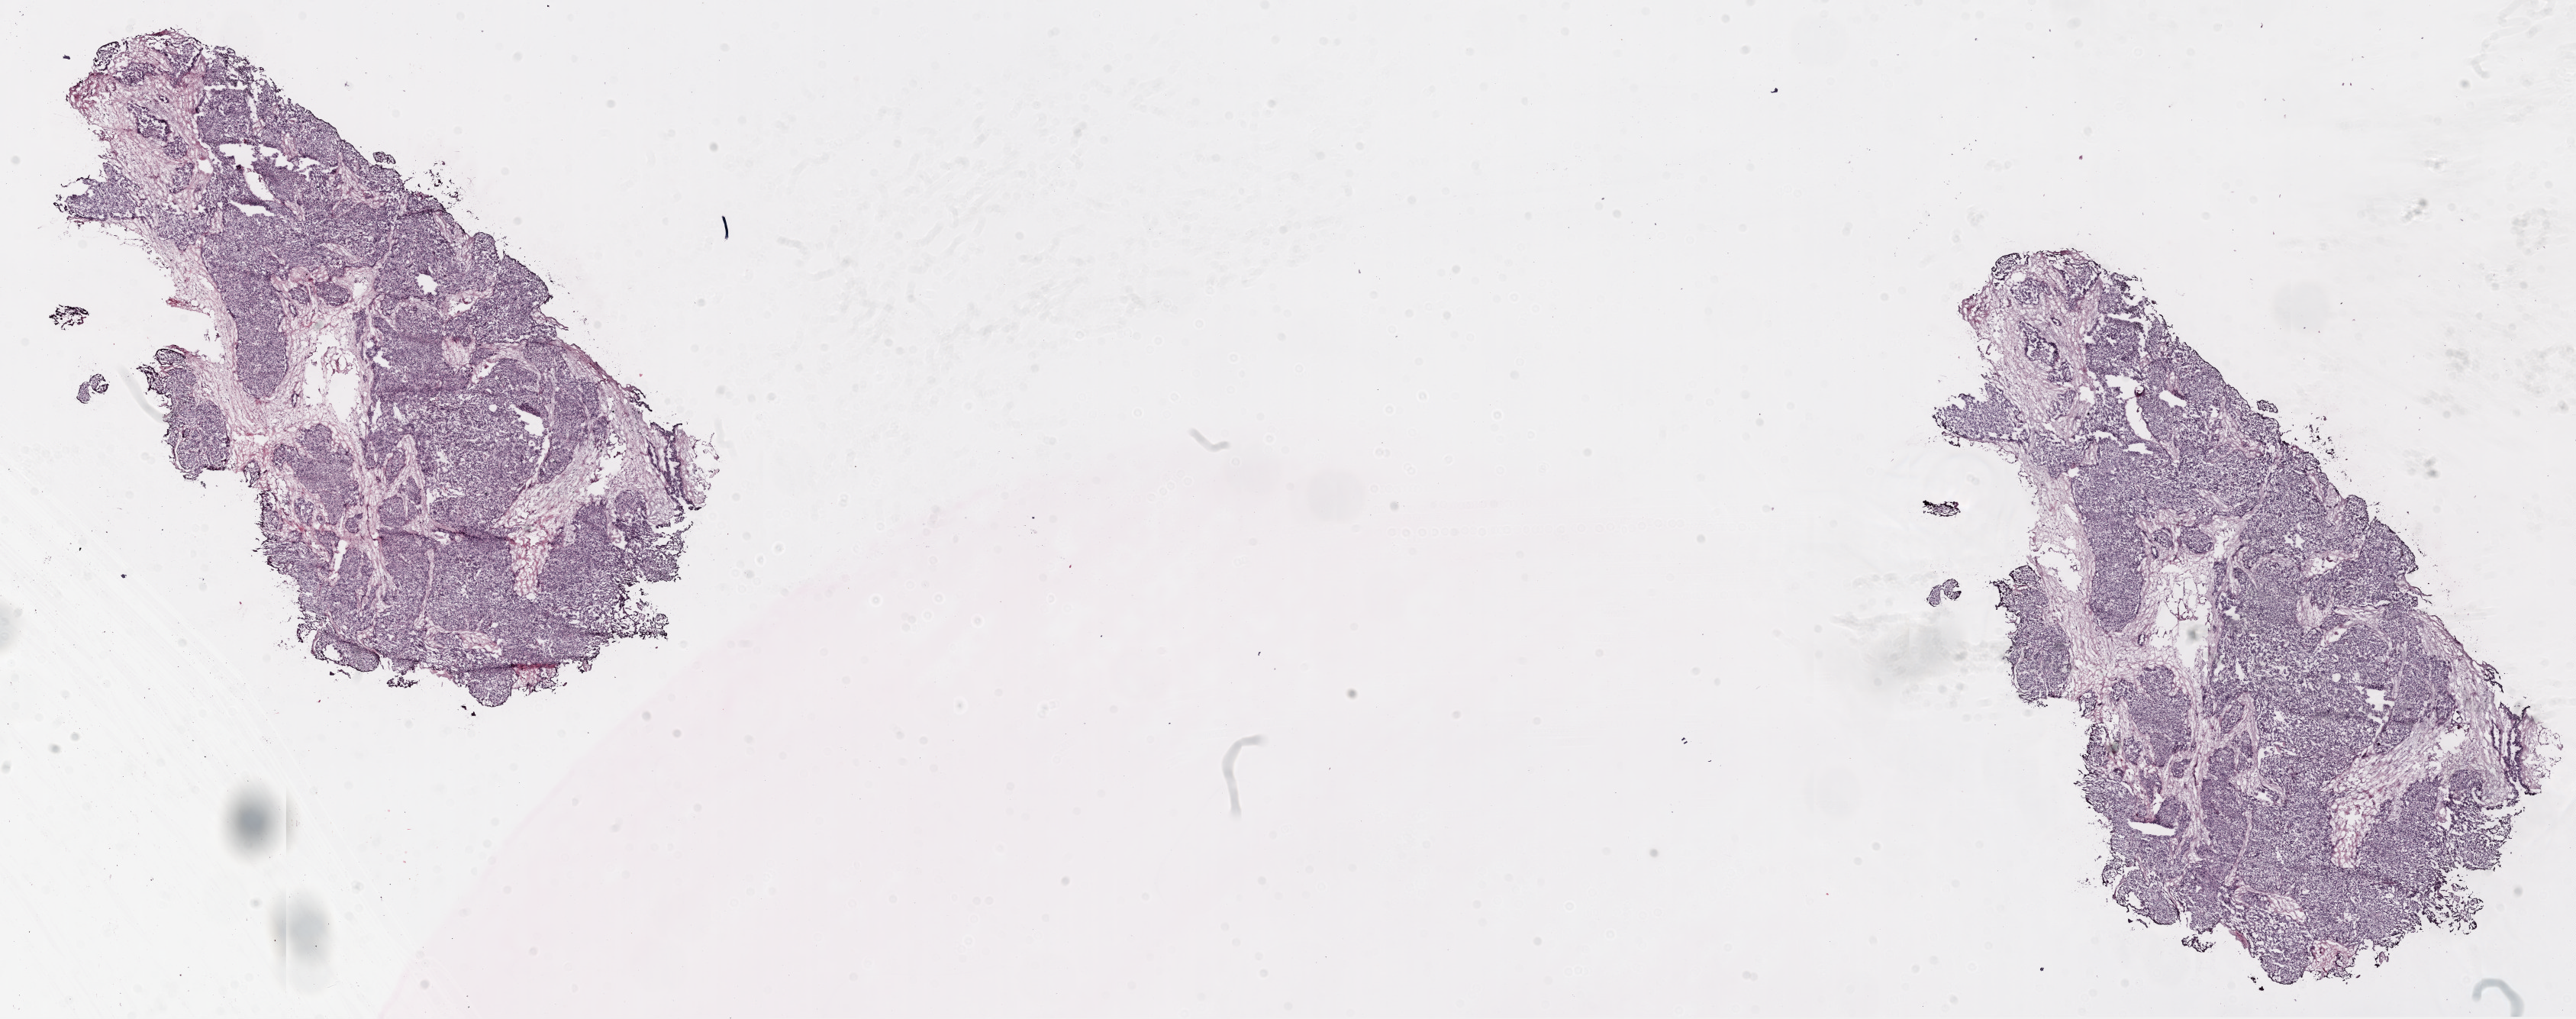
H&E whole-slide image — a low-resolution overview of the entire scanned area, about 27.1 x 10.7 mm (acquisition: 20x scan), frozen section from the top of the tissue portion, ovary, primary tumour sample. Female patient; age at initial diagnosis 59 years. Histologic grade: G2 (moderately differentiated). Slide review estimates, as recorded: tumour cells 80%, tumour nuclei 90%, normal cells 0%, stromal cells 20%, necrosis 0%.
* laterality: bilateral
* diagnosis: Serous cystadenocarcinoma, NOS
* FIGO stage: IIIC